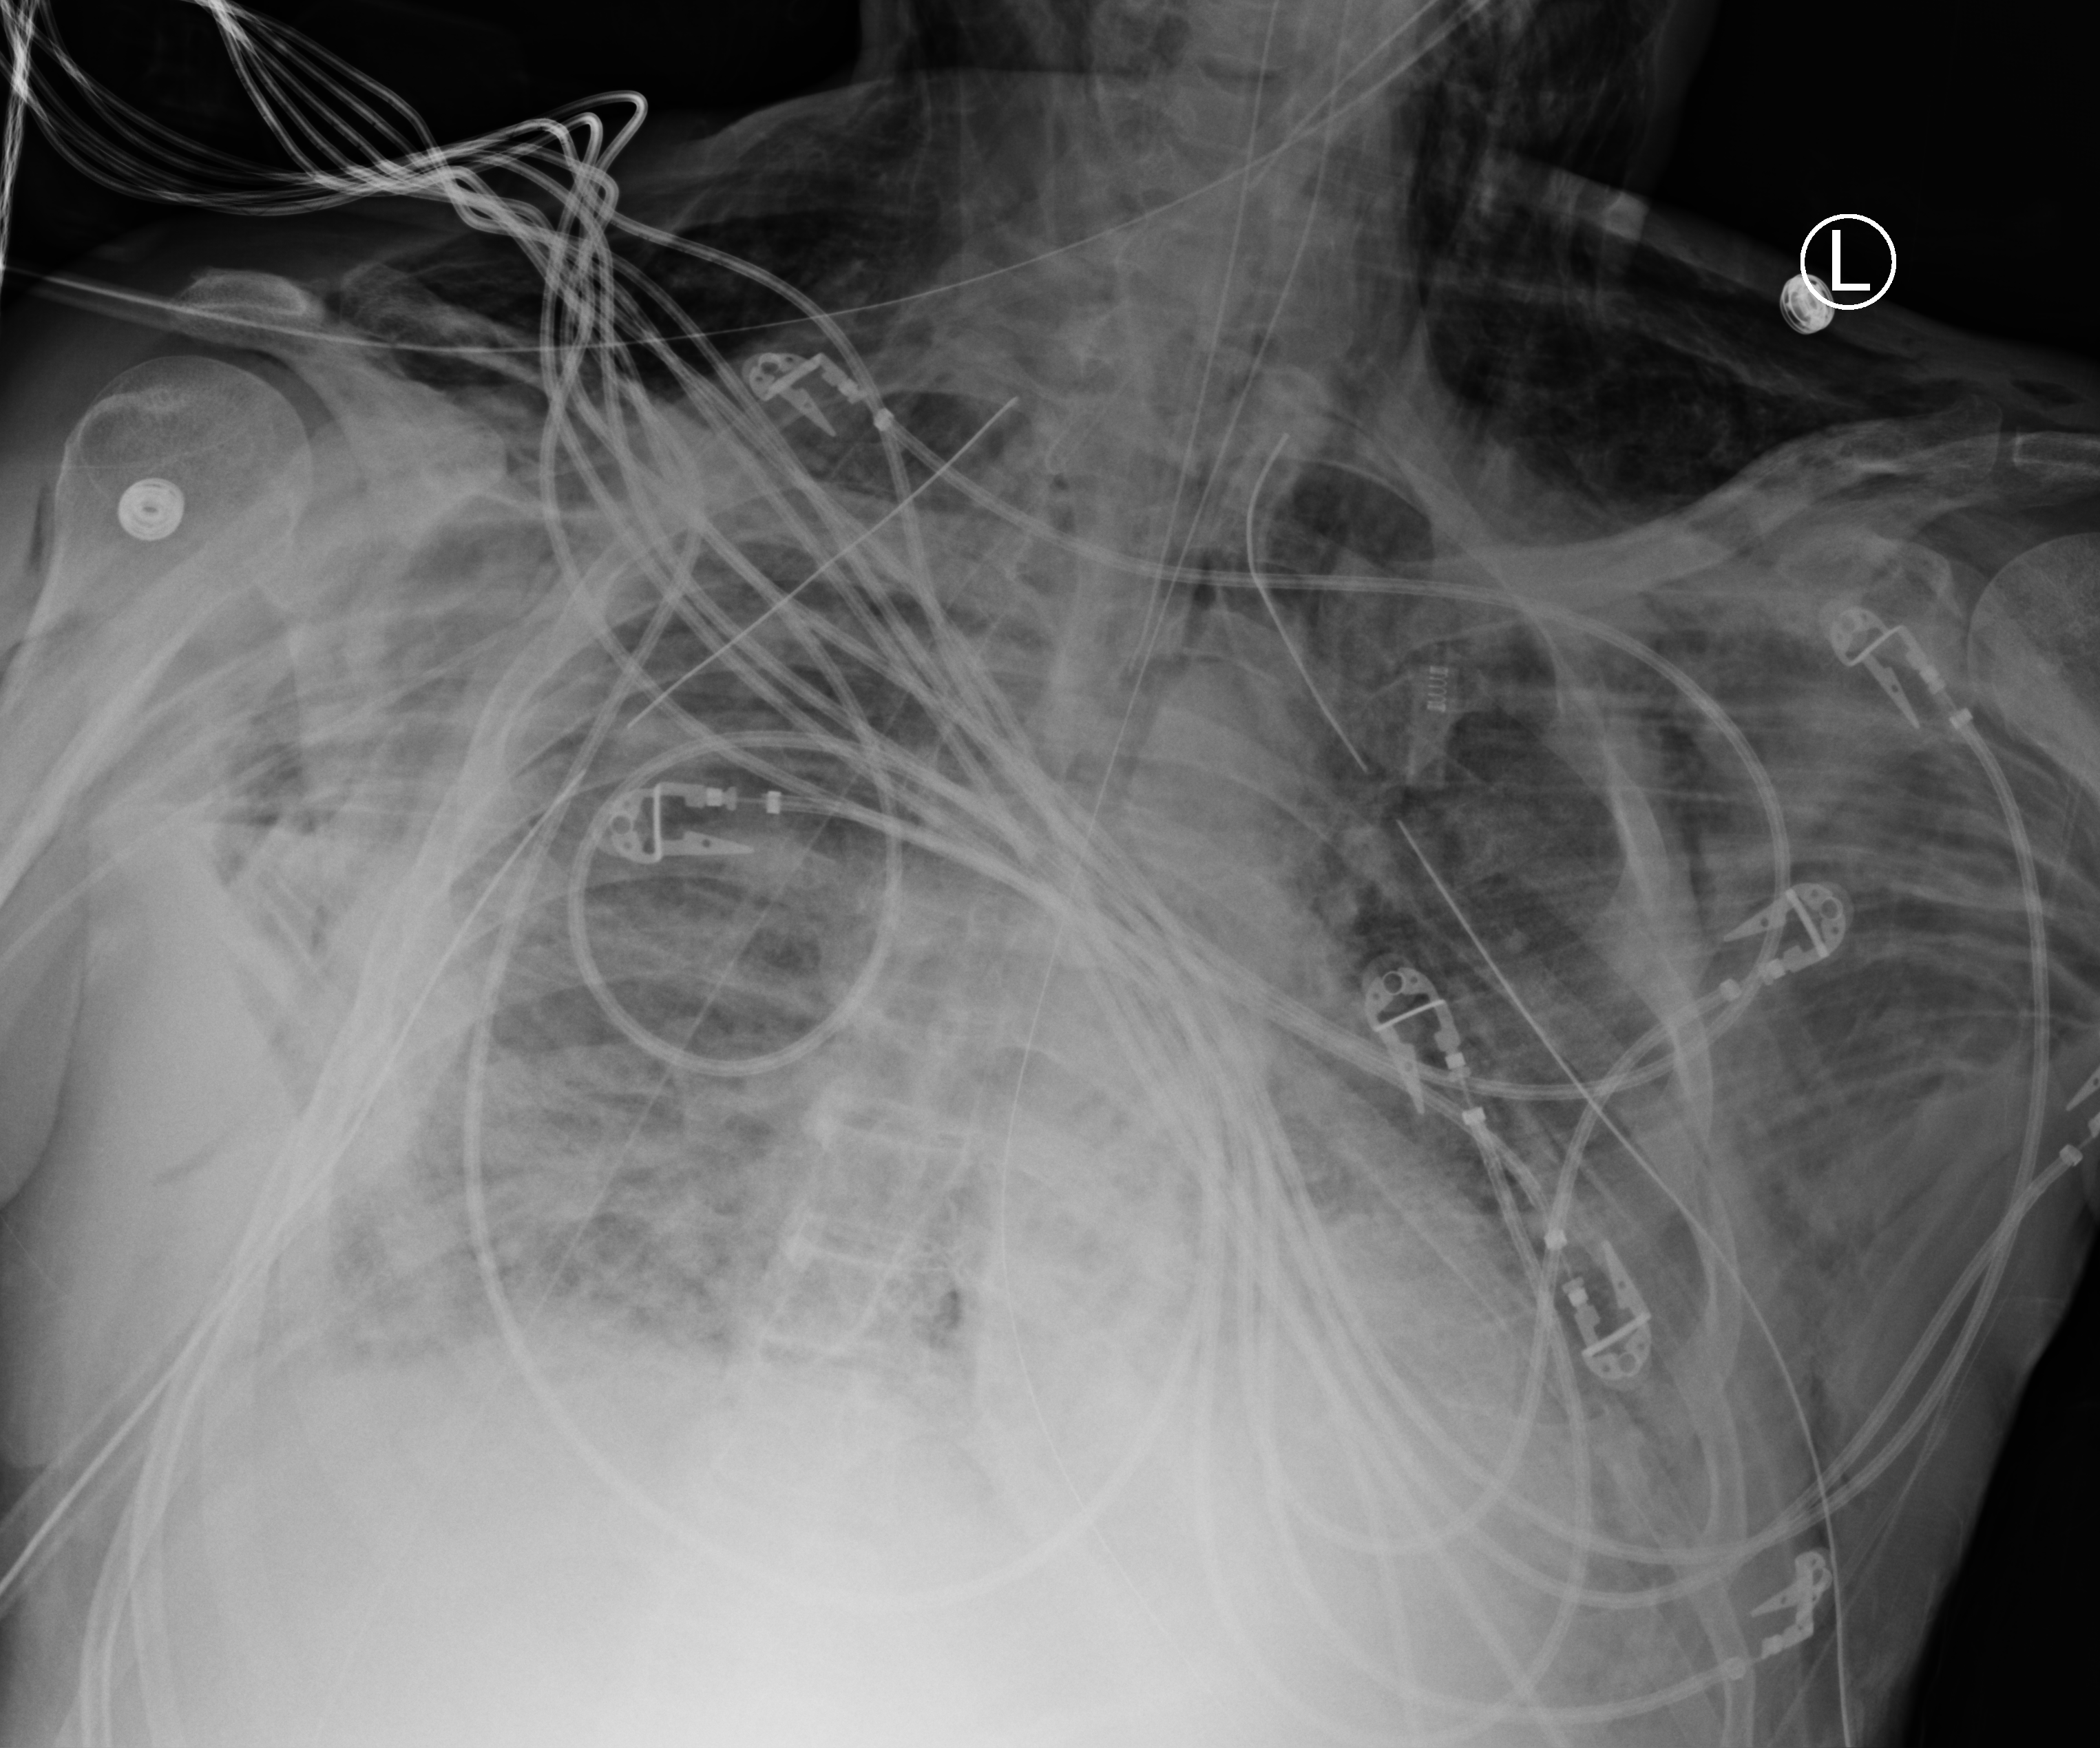
Bedside chest radiograph (computed radiography), anteroposterior (AP) projection. Patient hospitalised with COVID-19; male, aged 18–59 years.
Admission-level facts for this patient (not findings on this image; timing relative to this image not recorded): admitted to intensive care during this hospital stay: yes; mechanically ventilated during this hospital stay: yes.